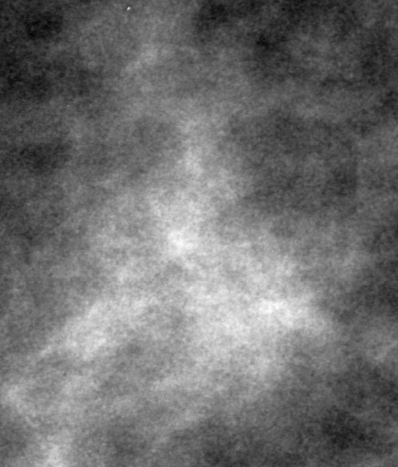
Region of interest cut from a scanned film mammogram (one marked finding), left breast, MLO view, BI-RADS breast density category 4 (scale 1–4).
Marked abnormality: mass, shape irregular, margins ill defined; BI-RADS assessment category 4; subtlety rating 3 on a 1 (subtle) to 5 (obvious) scale; pathology result (as recorded, not read from the image): benign.